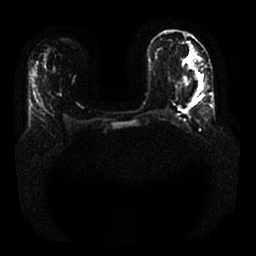
Breast MRI, one axial slice. Position 8 of 25 along the scan axis. Diffusion-weighted series; image 2 of 4 stored at this slice position (different b-values; order by instance number). 1.5 T. 256 × 256 image matrix, field of view 340 × 340 mm. Female patient.
Annotated regions visible in this slice (outlined manually by an expert reader):
- tumour on diffusion-weighted imaging: bounding box [x1, y1, x2, y2] px = [195, 89, 202, 98]